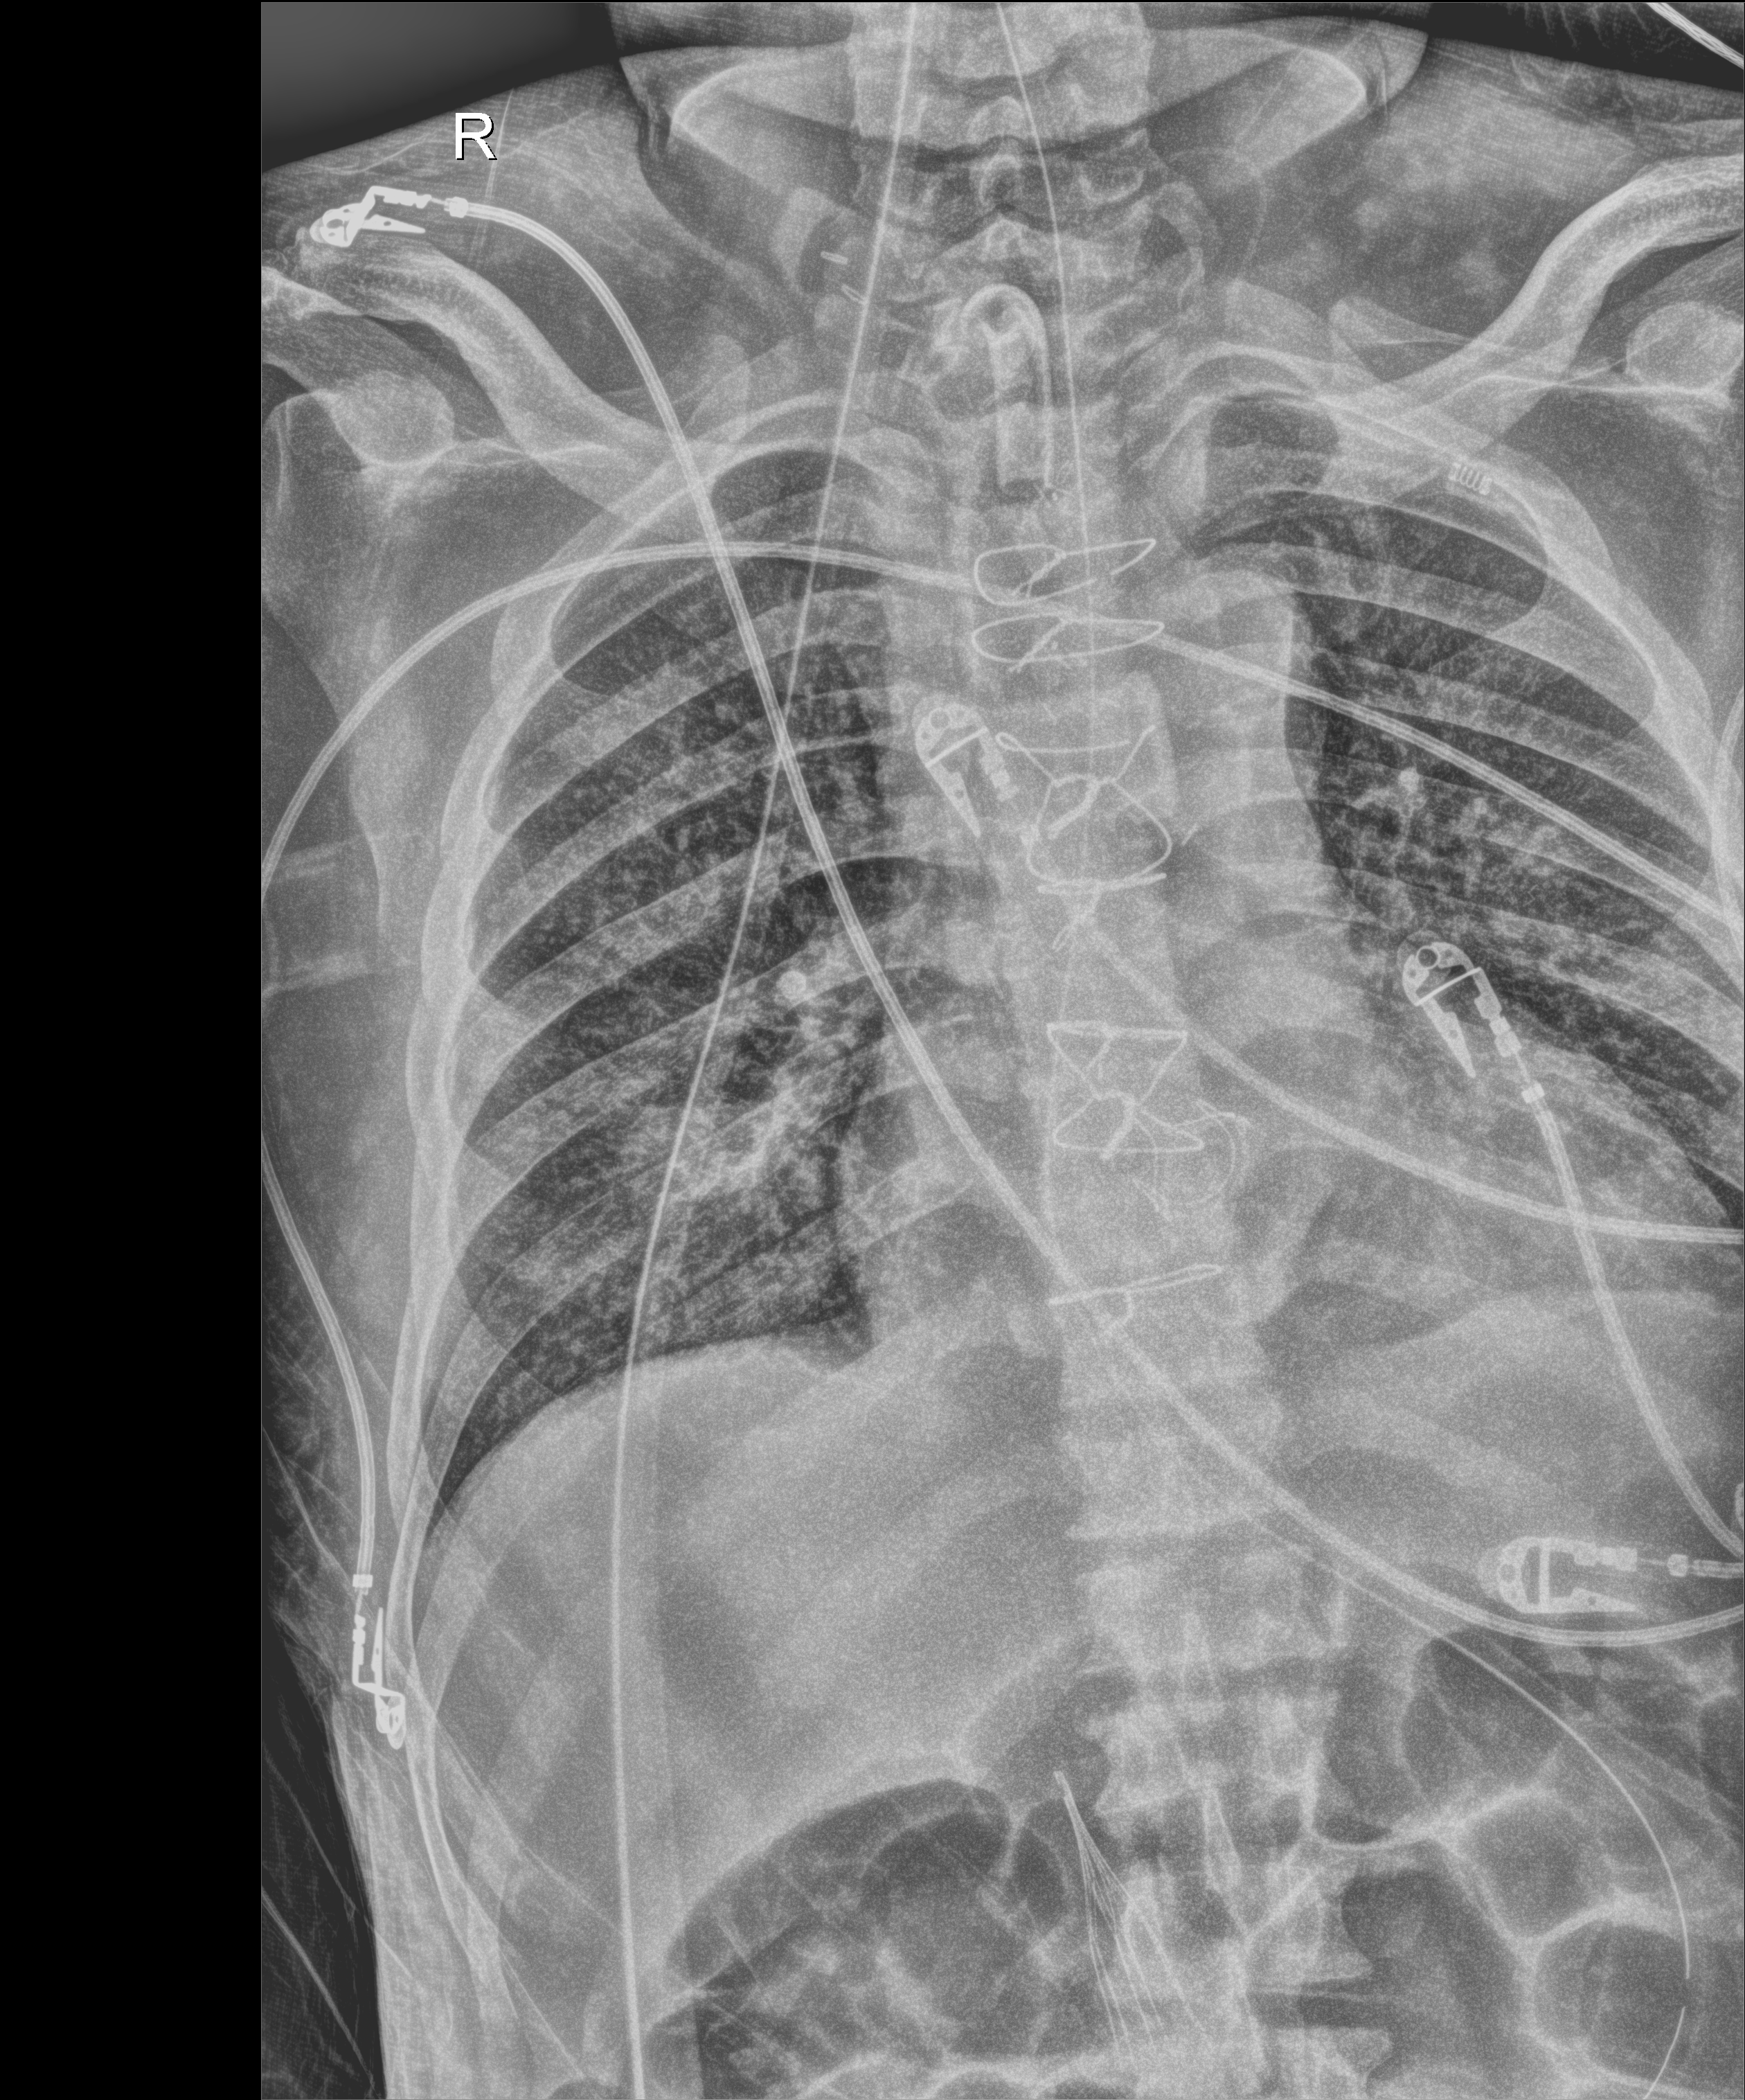
Portable chest radiograph; anteroposterior (AP) projection. Patient hospitalised with COVID-19; male, aged 60–74 years.
From the hospital-stay record, not from the radiograph (when in the stay this image was taken is not recorded): mechanically ventilated during this hospital stay: yes; admitted to intensive care during this hospital stay: yes; diabetes (admission record): no.